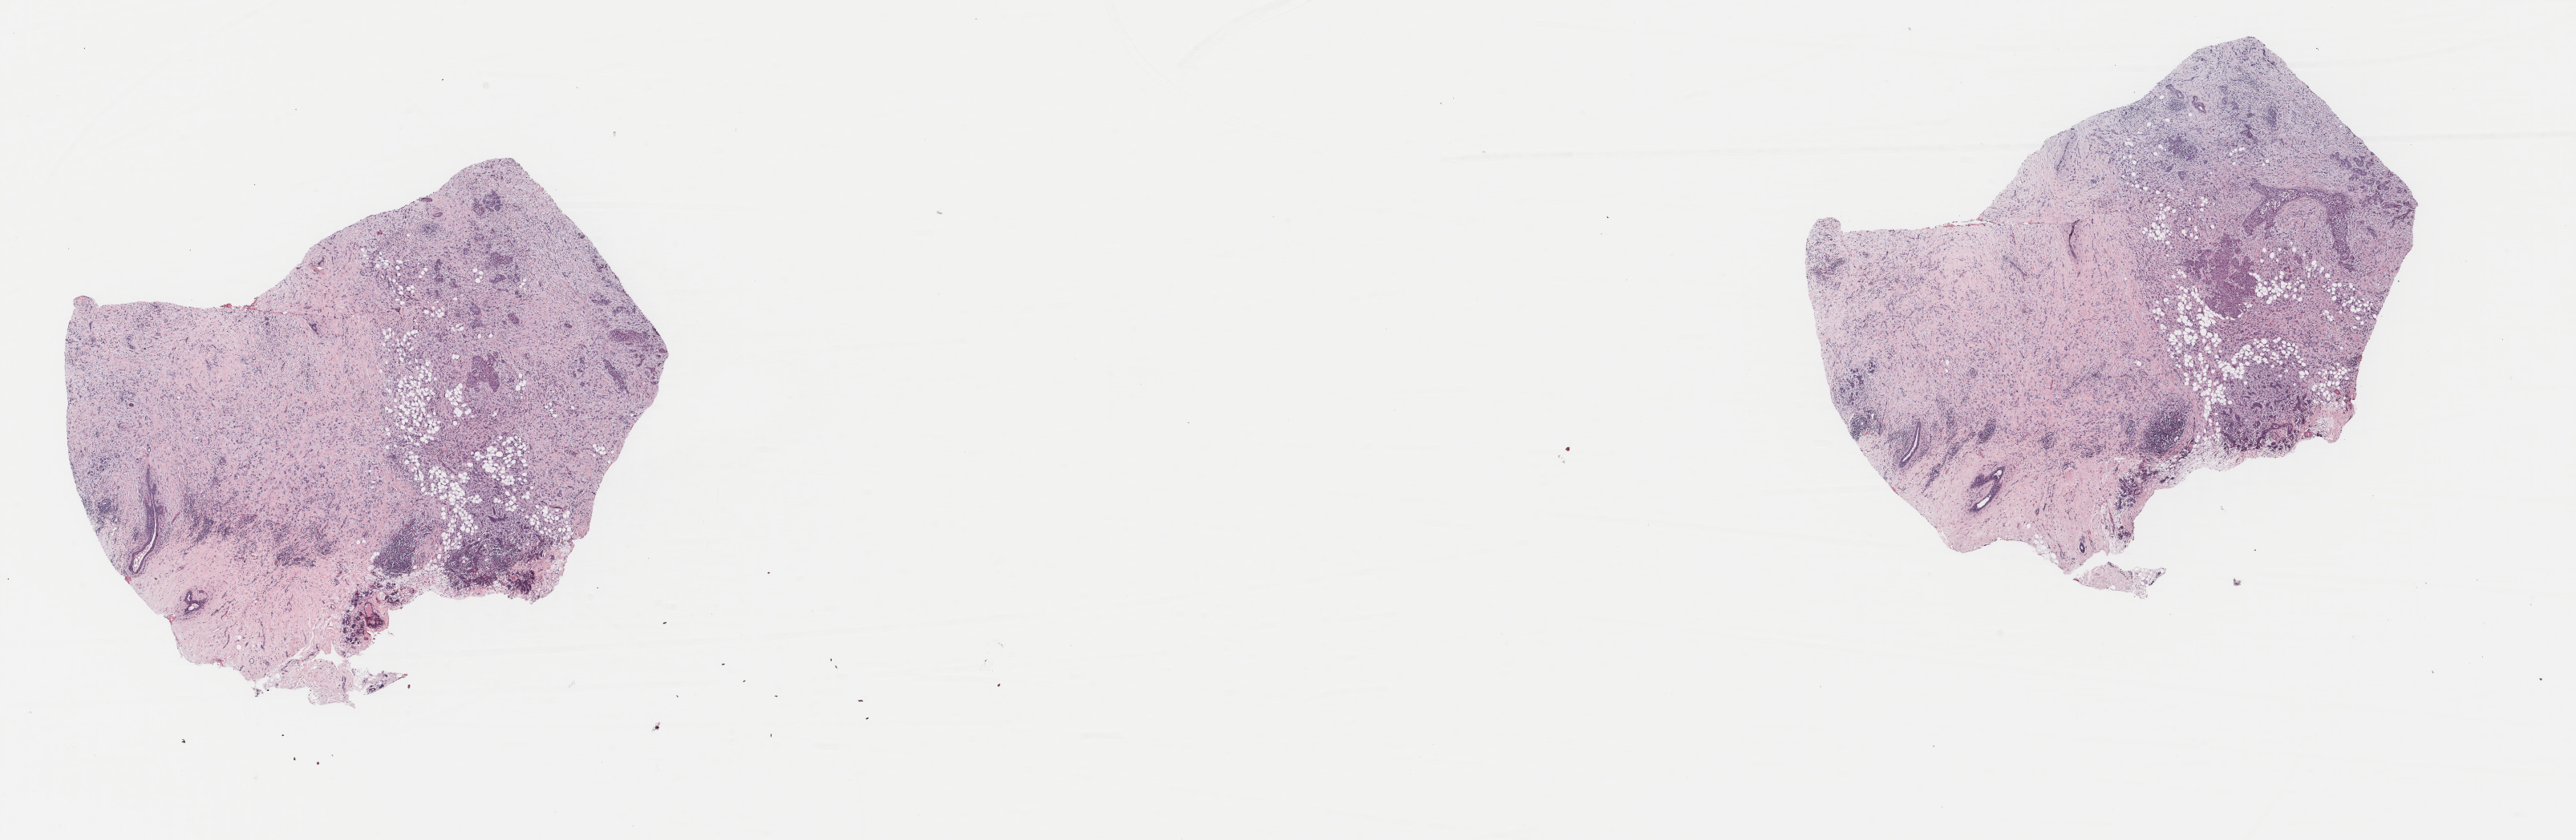
Whole-slide histology image, H&E-stained — a low-resolution overview of the entire scanned area, about 25.5 x 8.3 mm (from a 40x scan); formalin-fixed paraffin-embedded (FFPE) diagnostic section; sample: primary tumour, breast. Patient: female, age at initial diagnosis 40 years.
AJCC pathologic stage: IIB (7th edition). Histologic diagnosis: Lobular carcinoma, NOS.